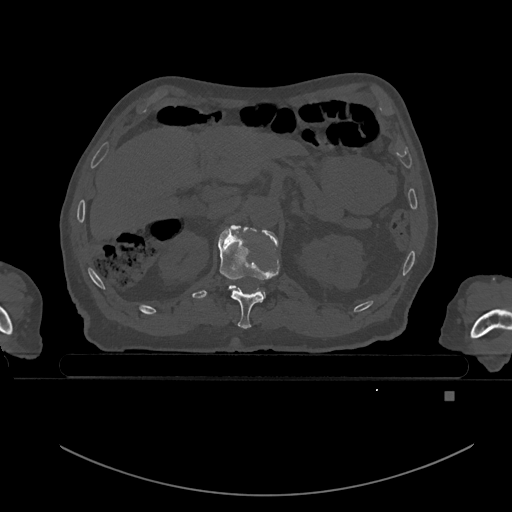
CT including the spine, one axial slice; slice 7 of 969 in the series (ordered by position); bone window (W 1800 / L 400 HU); 0.5 mm slice thickness; 512 × 512 image matrix, field of view 456 × 456 mm. Patient: male, 82 years. Case-level facts recorded for this patient, not image findings: primary cancer: prostate.
Structures marked on this image (semi-automatically segmented with operator editing):
- T11 vertebra: bounding box <218,227,280,329> (left, top, right, bottom; pixels)